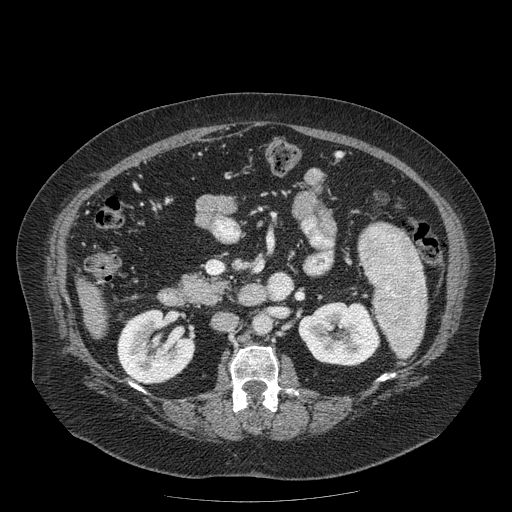
Contrast-enhanced abdominal CT (liver protocol), one axial slice. Position 53 of 204 along the scan axis. Reconstruction kernel STANDARD. 120 kVp. Soft-tissue window (W 400 / L 40 HU). 2.5 mm slice thickness. 512 × 512 image matrix, field of view 440 × 440 mm. Case-level facts recorded for this patient, not image findings: diagnosis: hepatocellular carcinoma (patient treated with transarterial chemoembolisation; whether this scan precedes or follows treatment is not stated here); TNM stage (as recorded): Stage-IIIB; Child-Pugh class: A; tumour nodularity: uninodular.
Structures marked on this image (semi-automatically segmented with operator editing):
- liver parenchyma outside the tumour (the mass and vessels are separate outlines, so this box may not span the whole liver): bounding box (x1, y1, x2, y2) in pixels: (78, 278, 106, 338)